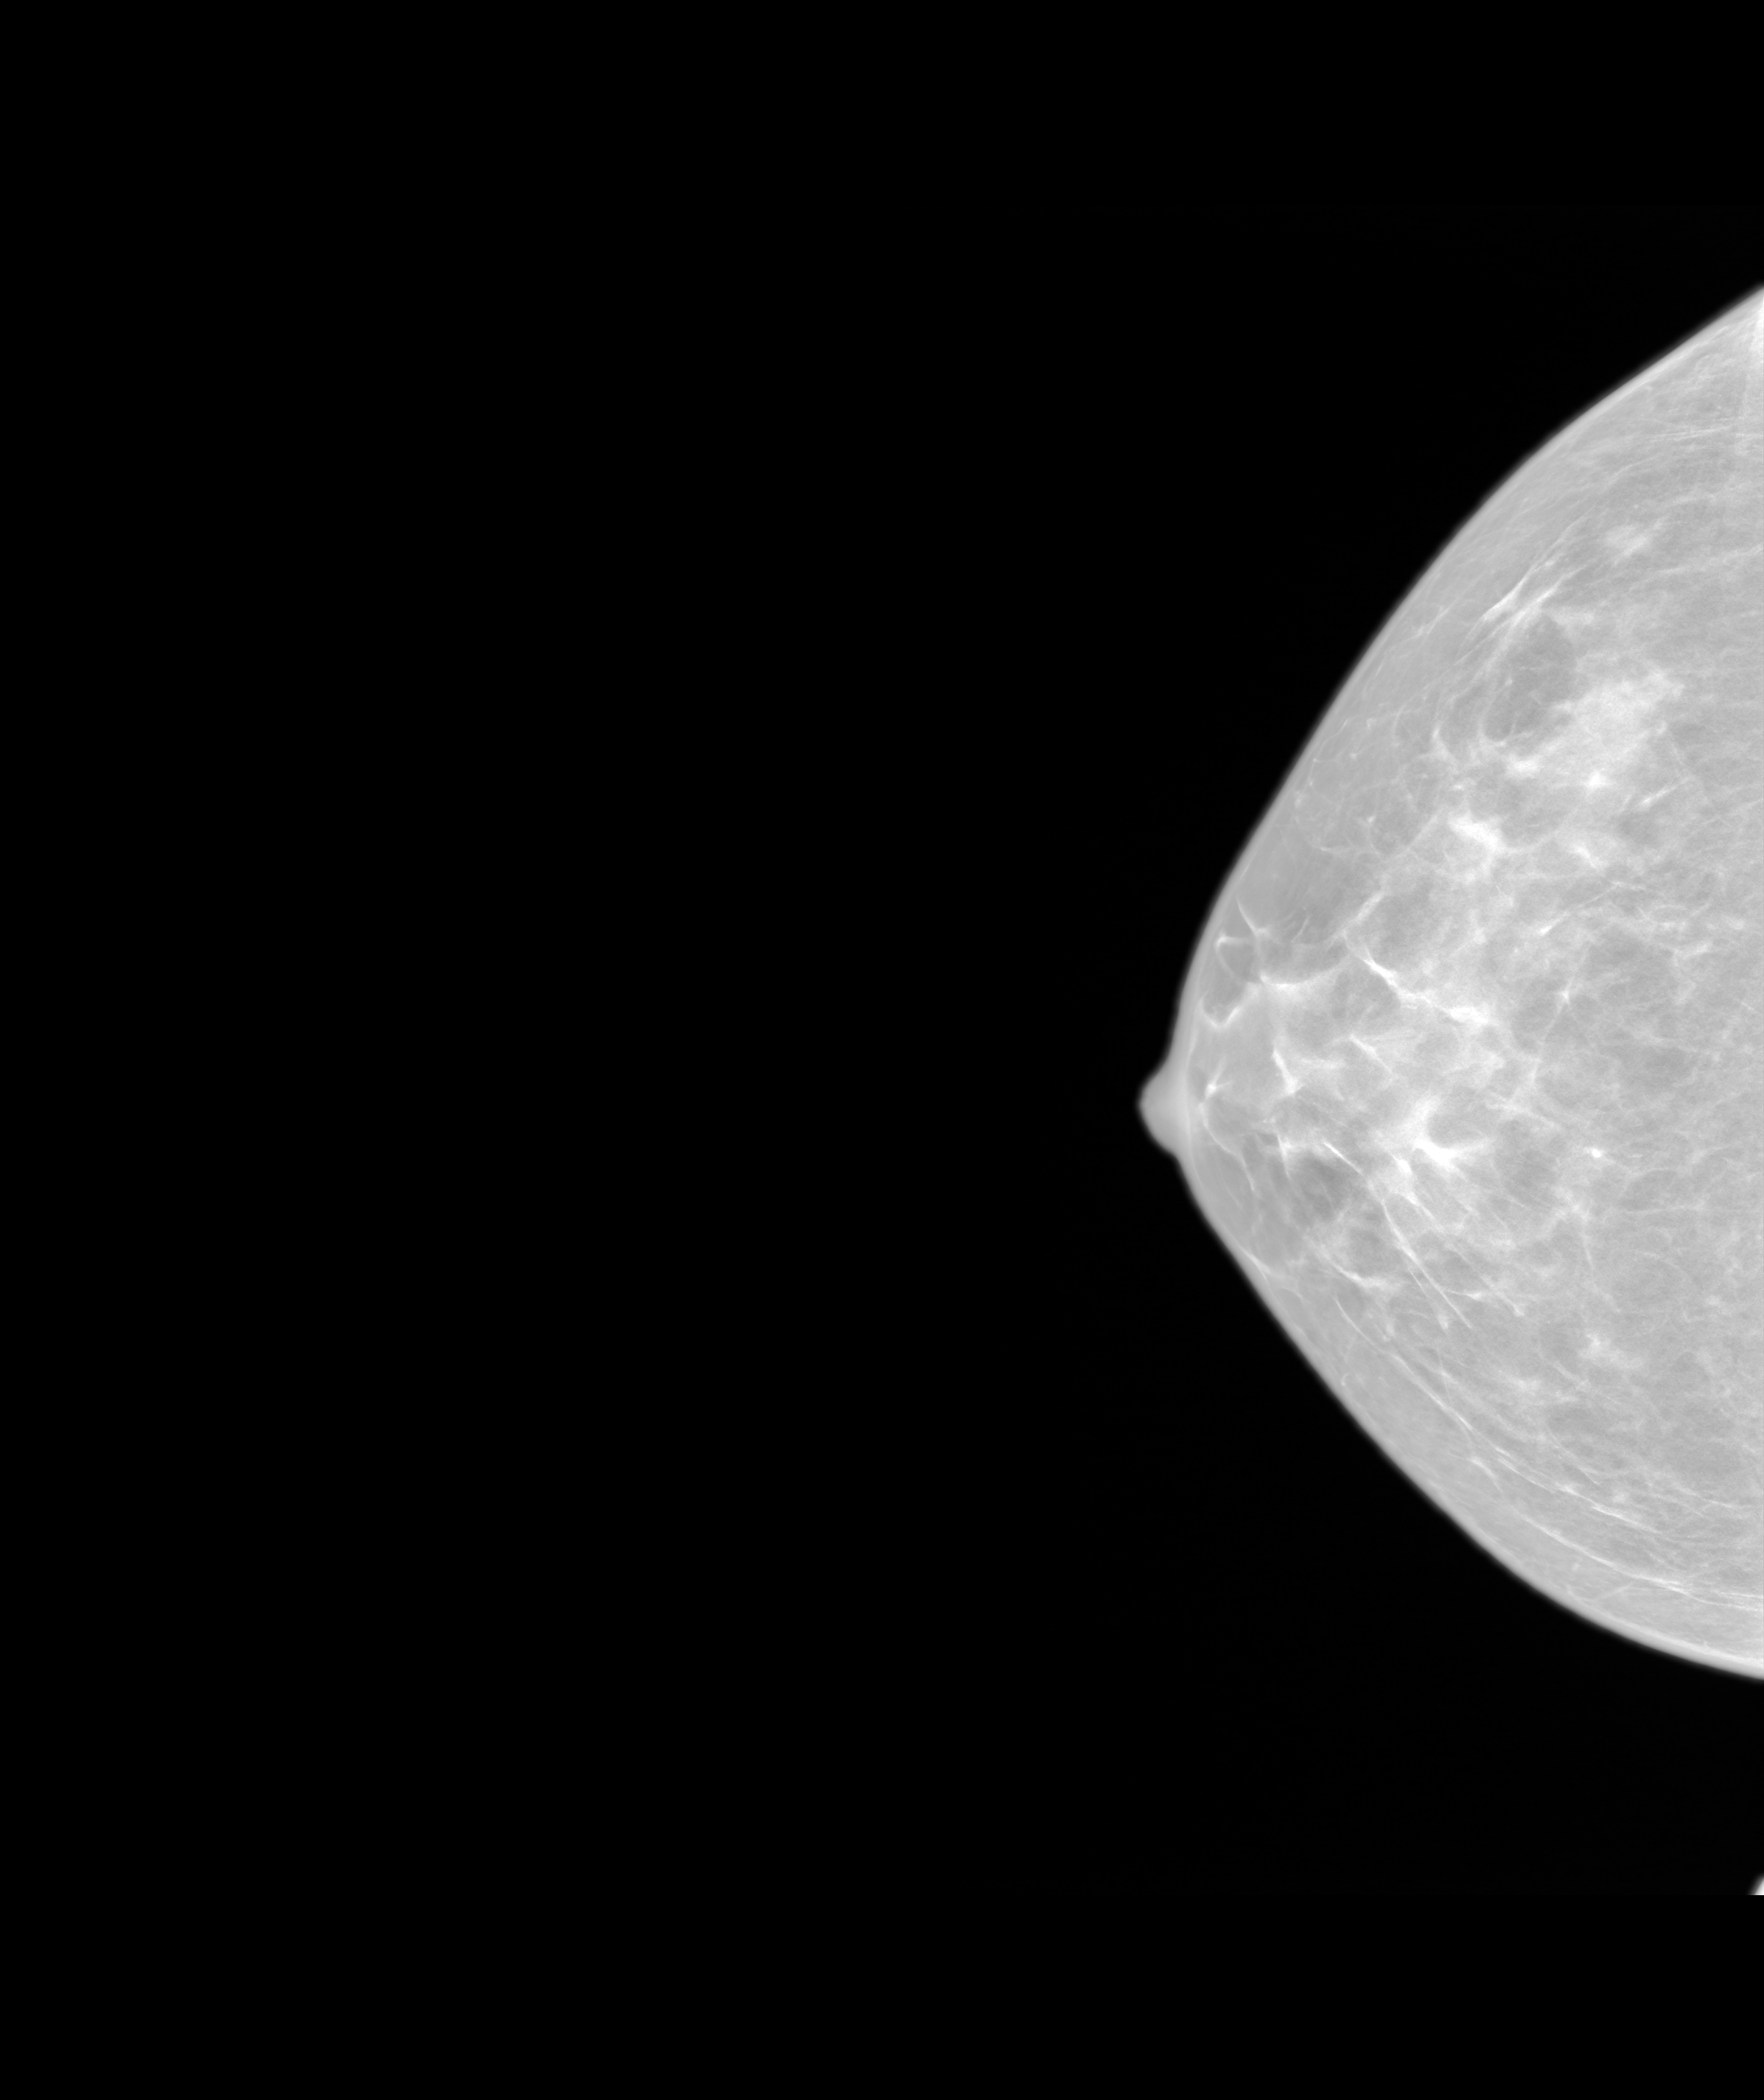
Annual screening mammography examination; system: SenoIris_1SP1.1(421). Patient aged 44 years (female).
Image type: synthesized 2-D view from tomosynthesis. Breast: right. Projection: craniocaudal (CC) view.